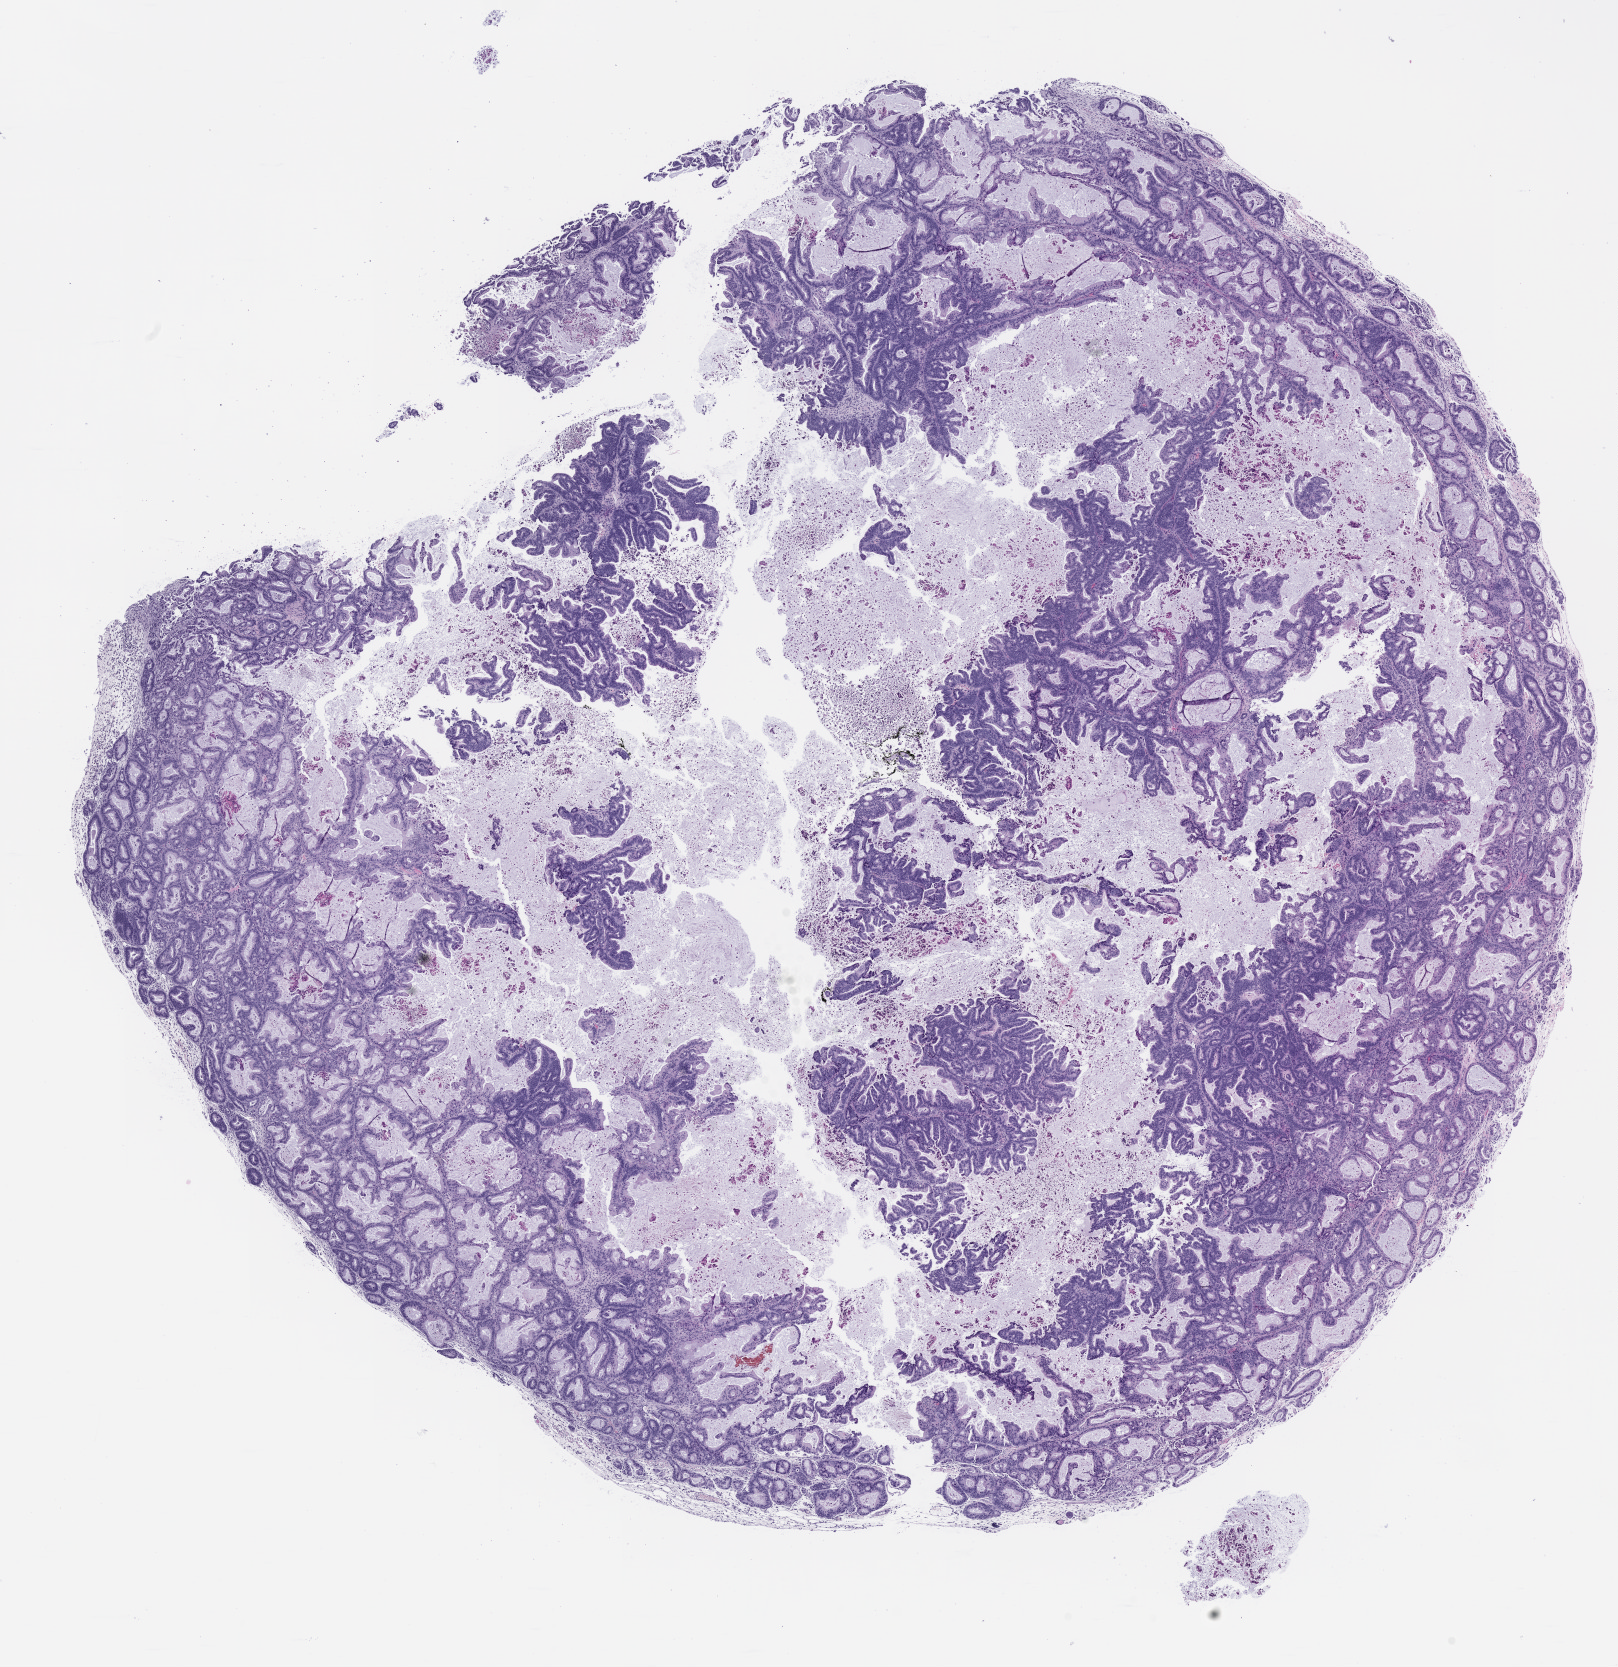
Hematoxylin and eosin (H&E) whole-slide image of a patient-derived xenograft (PDX) tumor grown in a mouse, passage 1, whole scanned area (about 13.0 x 13.4 mm) shown as a low-resolution overview; formalin-fixed paraffin-embedded section; tumor site category: pancreas.
• originating patient diagnosis: Pancreatic Adenocarcinoma